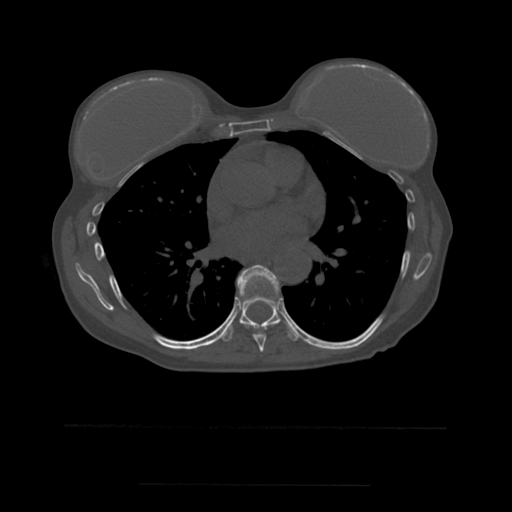
CT including the spine, one axial slice. Slice 348 of 544 in the series (ordered by position). Bone window (W 1800 / L 400 HU). 1.25 mm slice thickness. 512 × 512 image matrix, field of view 350 × 350 mm. Patient age 58 years. From the clinical record (not read from this slice): primary cancer: lung.
Structures marked on this image (semi-automatic segmentation, software-assisted and operator-edited):
- T7 vertebra: box from (x=237, y=265) to (x=279, y=352) px
- T8 vertebra: (x=221, y=291)–(x=297, y=342)